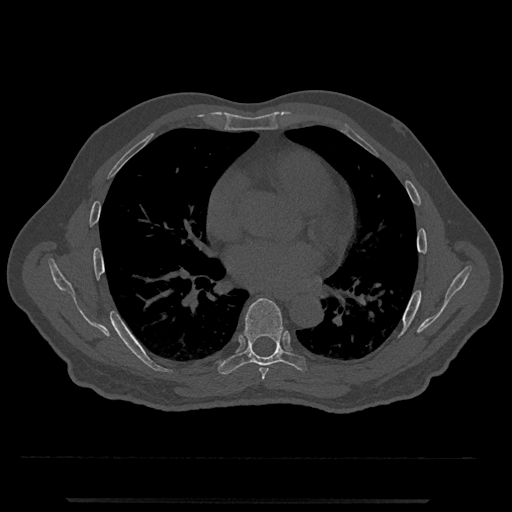
CT including the spine, one axial slice; reconstruction kernel Br40s/3; bone window (W 1800 / L 400 HU); 0.5 mm slice thickness; 512 × 512 image matrix, field of view 419 × 419 mm. Male patient, age 63 years. From the clinical record (not read from this slice): primary cancer: prostate.
Structures marked on this image (semi-automatic segmentation, software-assisted and operator-edited):
- T6 vertebra: bounding box (x1, y1, x2, y2) in pixels: (259, 367, 268, 380)
- T7 vertebra: (218, 298, 307, 375)